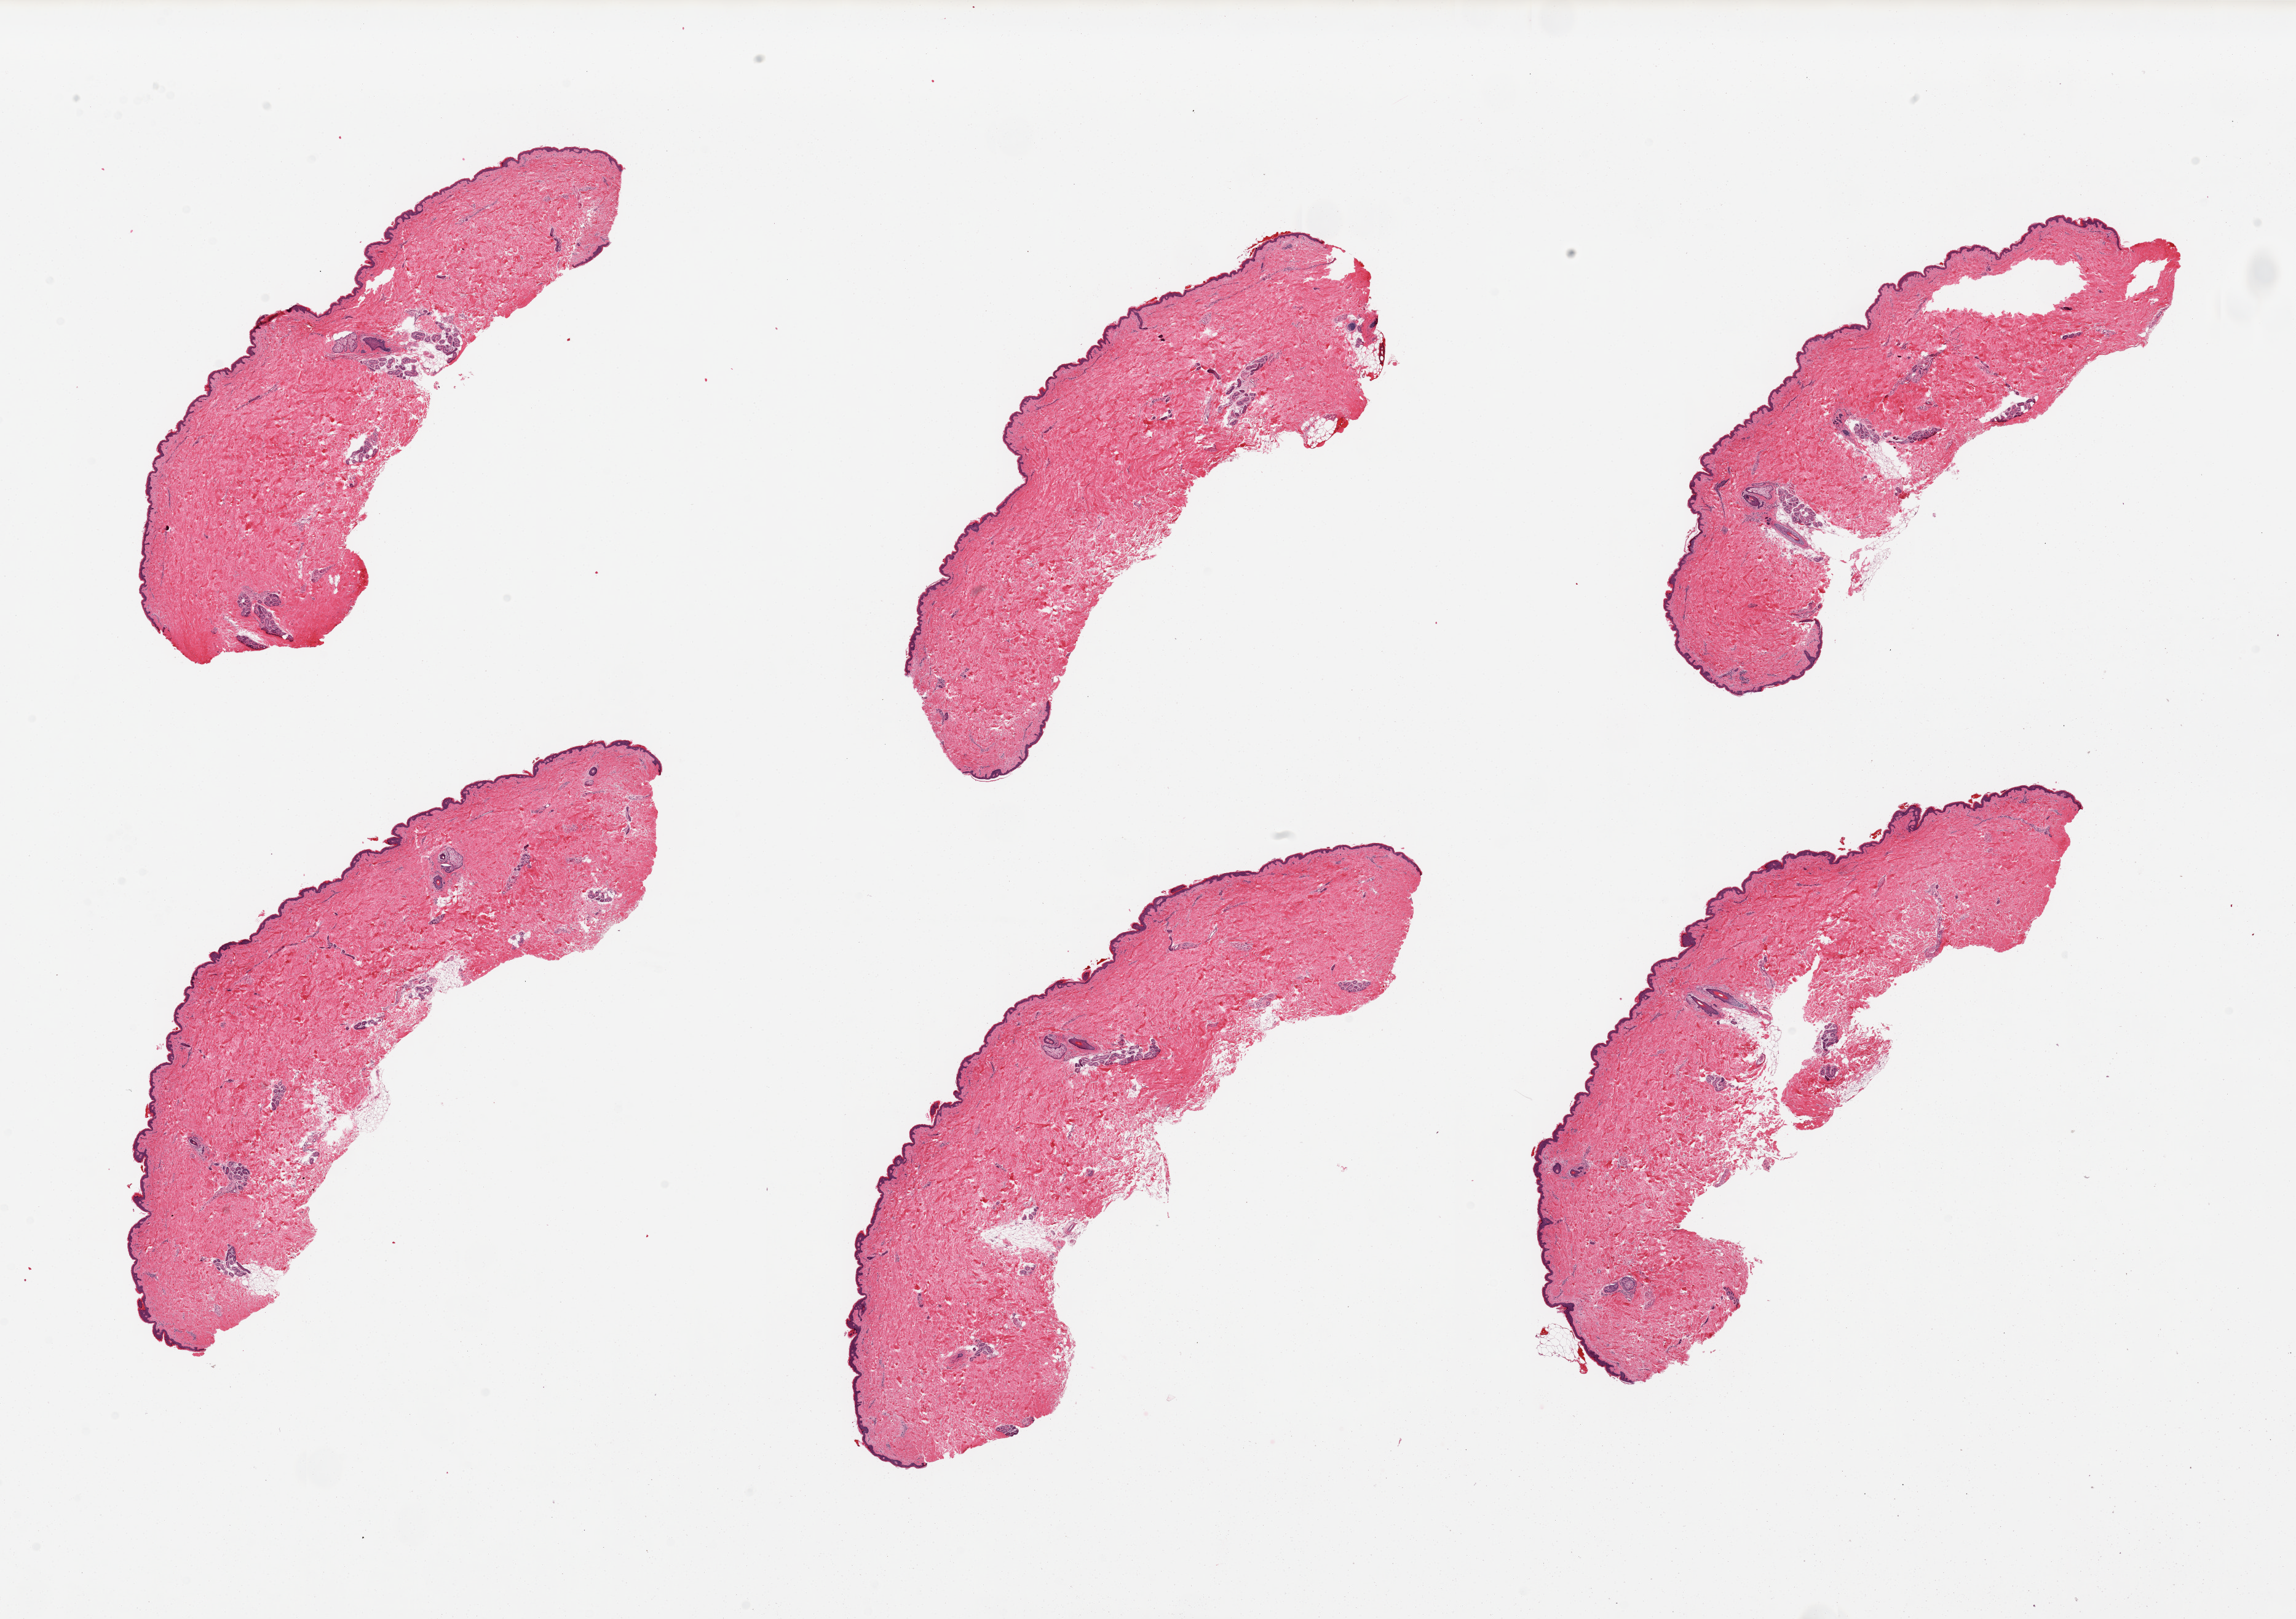
Digitized haematoxylin and eosin-stained section, brightfield, shown as a low-resolution overview of the whole scanned area (about 29.5 x 20.8 mm), PAXgene-fixed paraffin-embedded (PFPE) section, sampled site (target tissue): skin of suprapubic region, donor tissue sample. Donor: female.
Pathologist's review note for this sample: 6 pieces; squamous epithelium is 35-45 microns thick. Minimal adherent dermal fat.